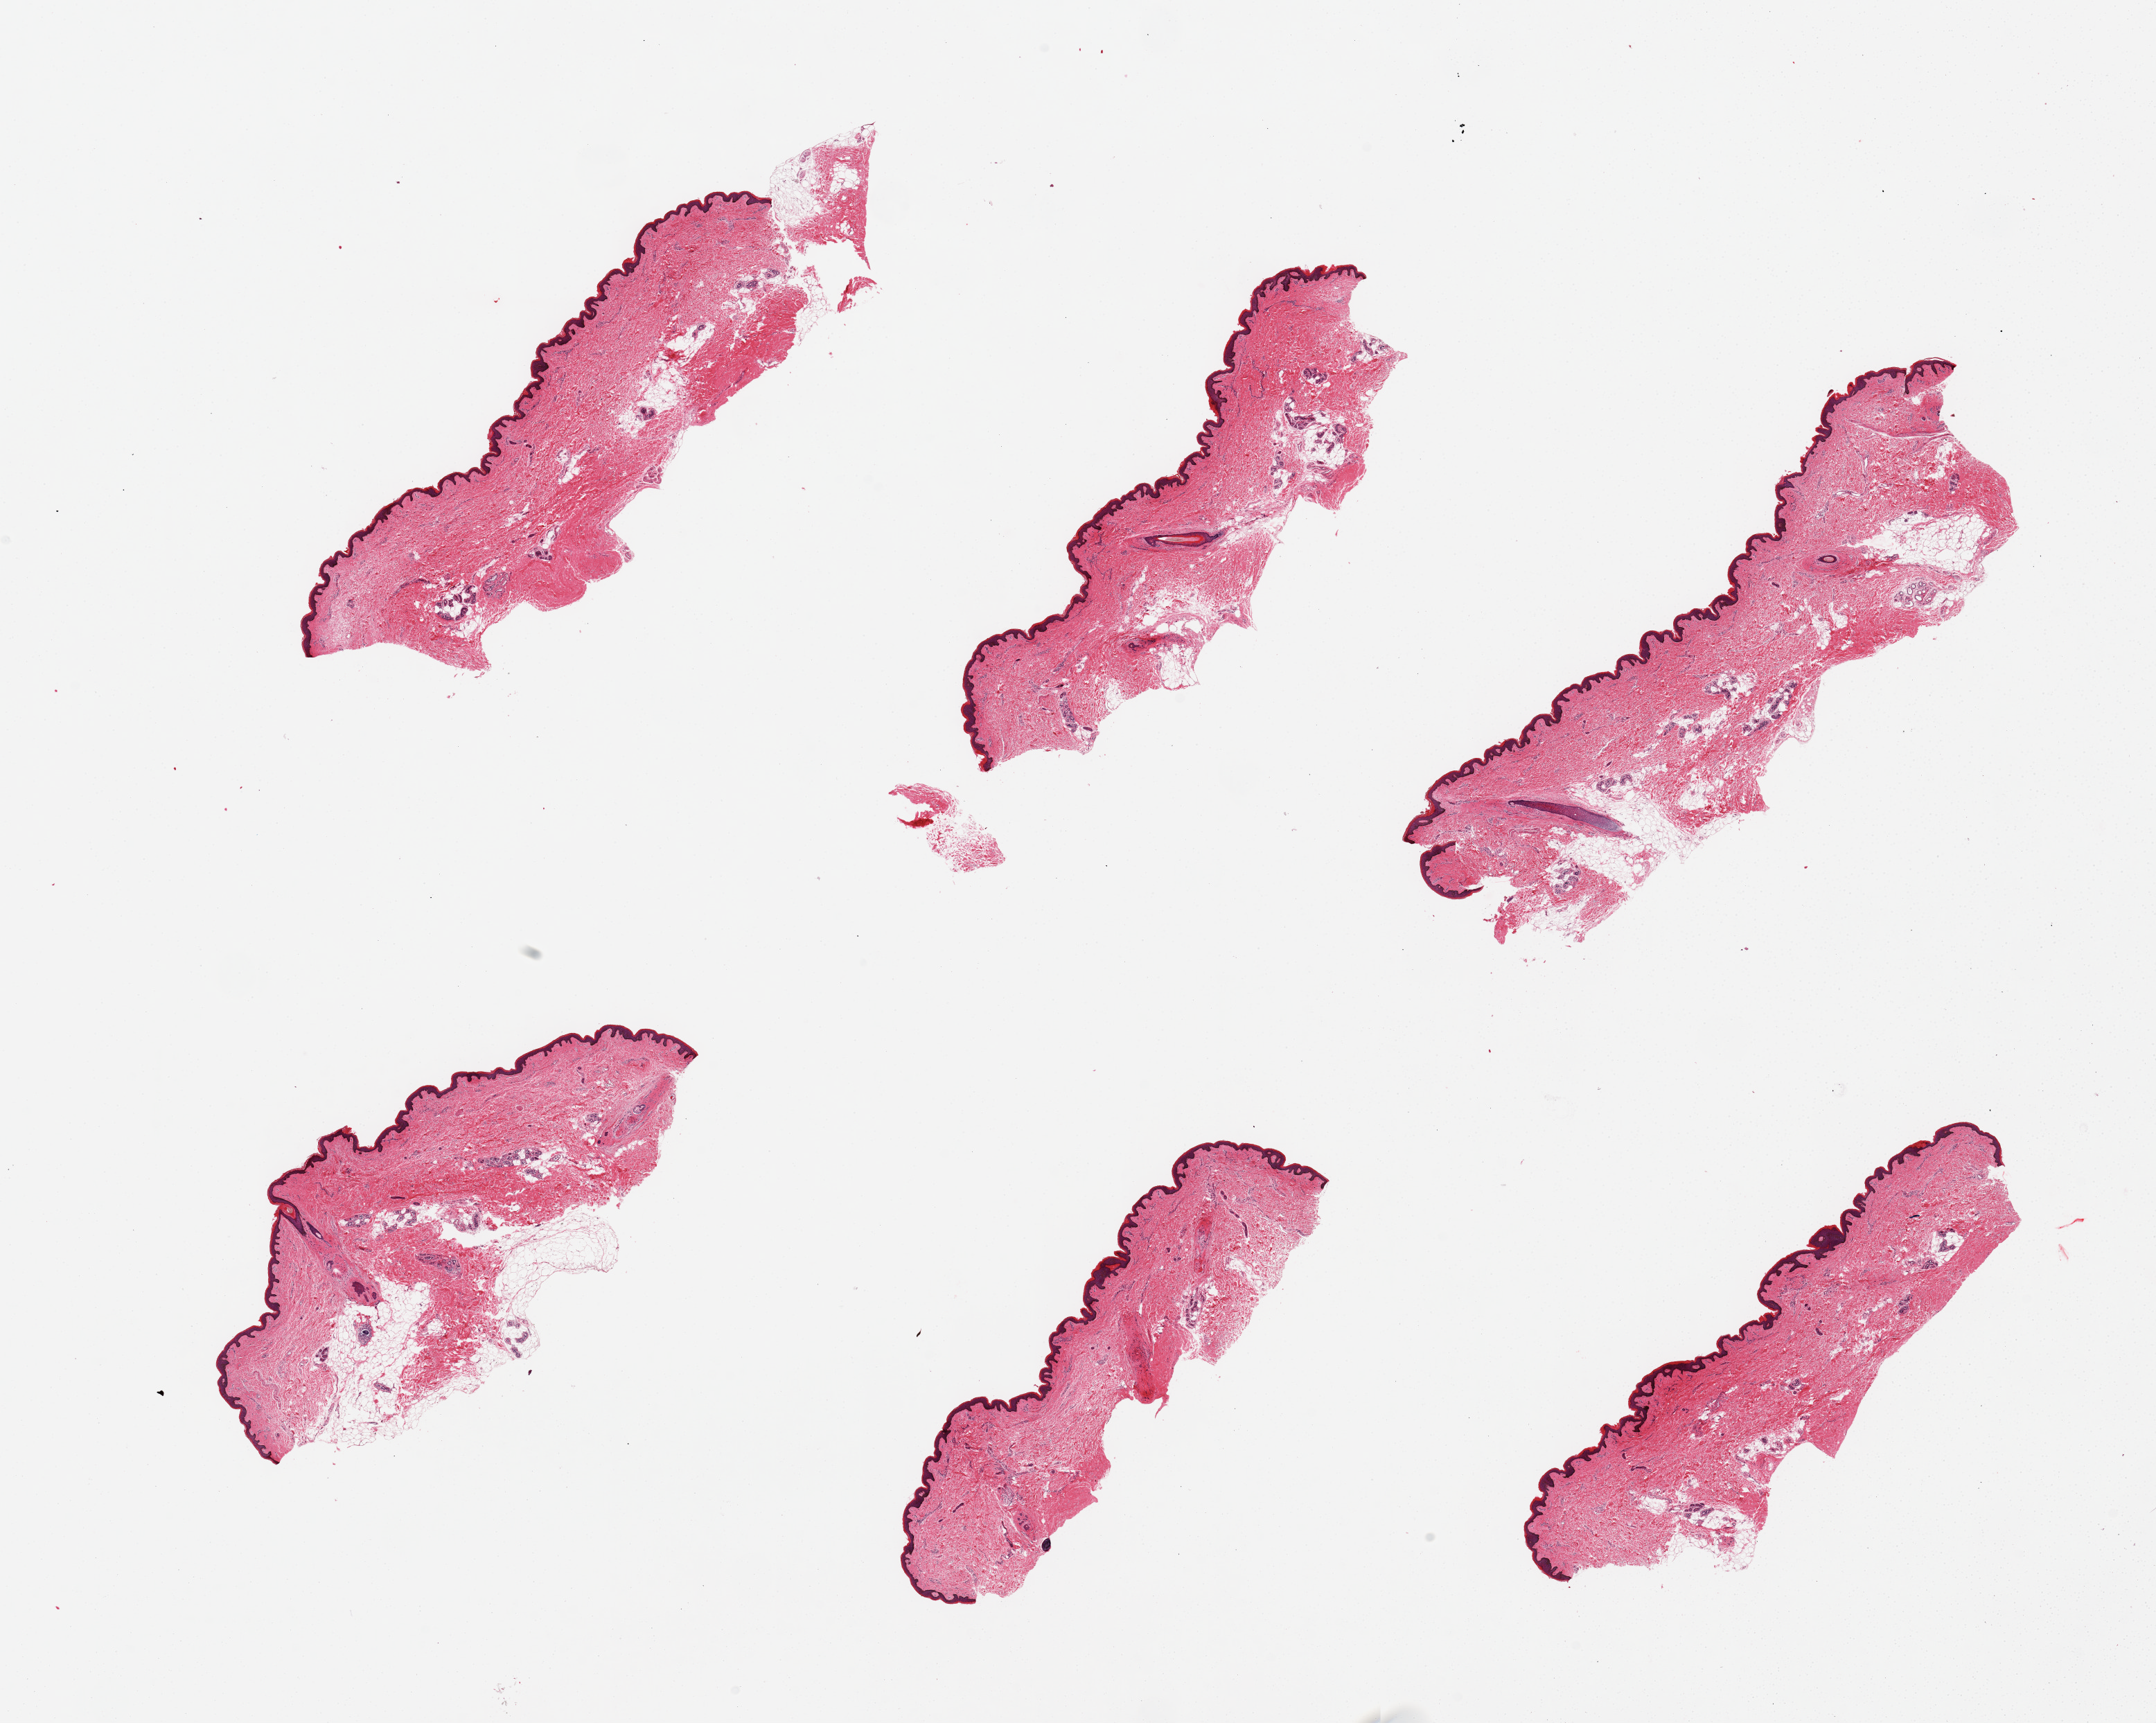
H&E whole-slide image, shown as a low-resolution overview of the whole scanned area (about 24.6 x 19.7 mm, from a 20x scan), PAXgene-fixed paraffin-embedded (PFPE) section, target tissue: skin of suprapubic region, tissue donor sample. Donor: female.
• review note (as recorded): 6 pieces; squamous epithelium is ~60 microns thick